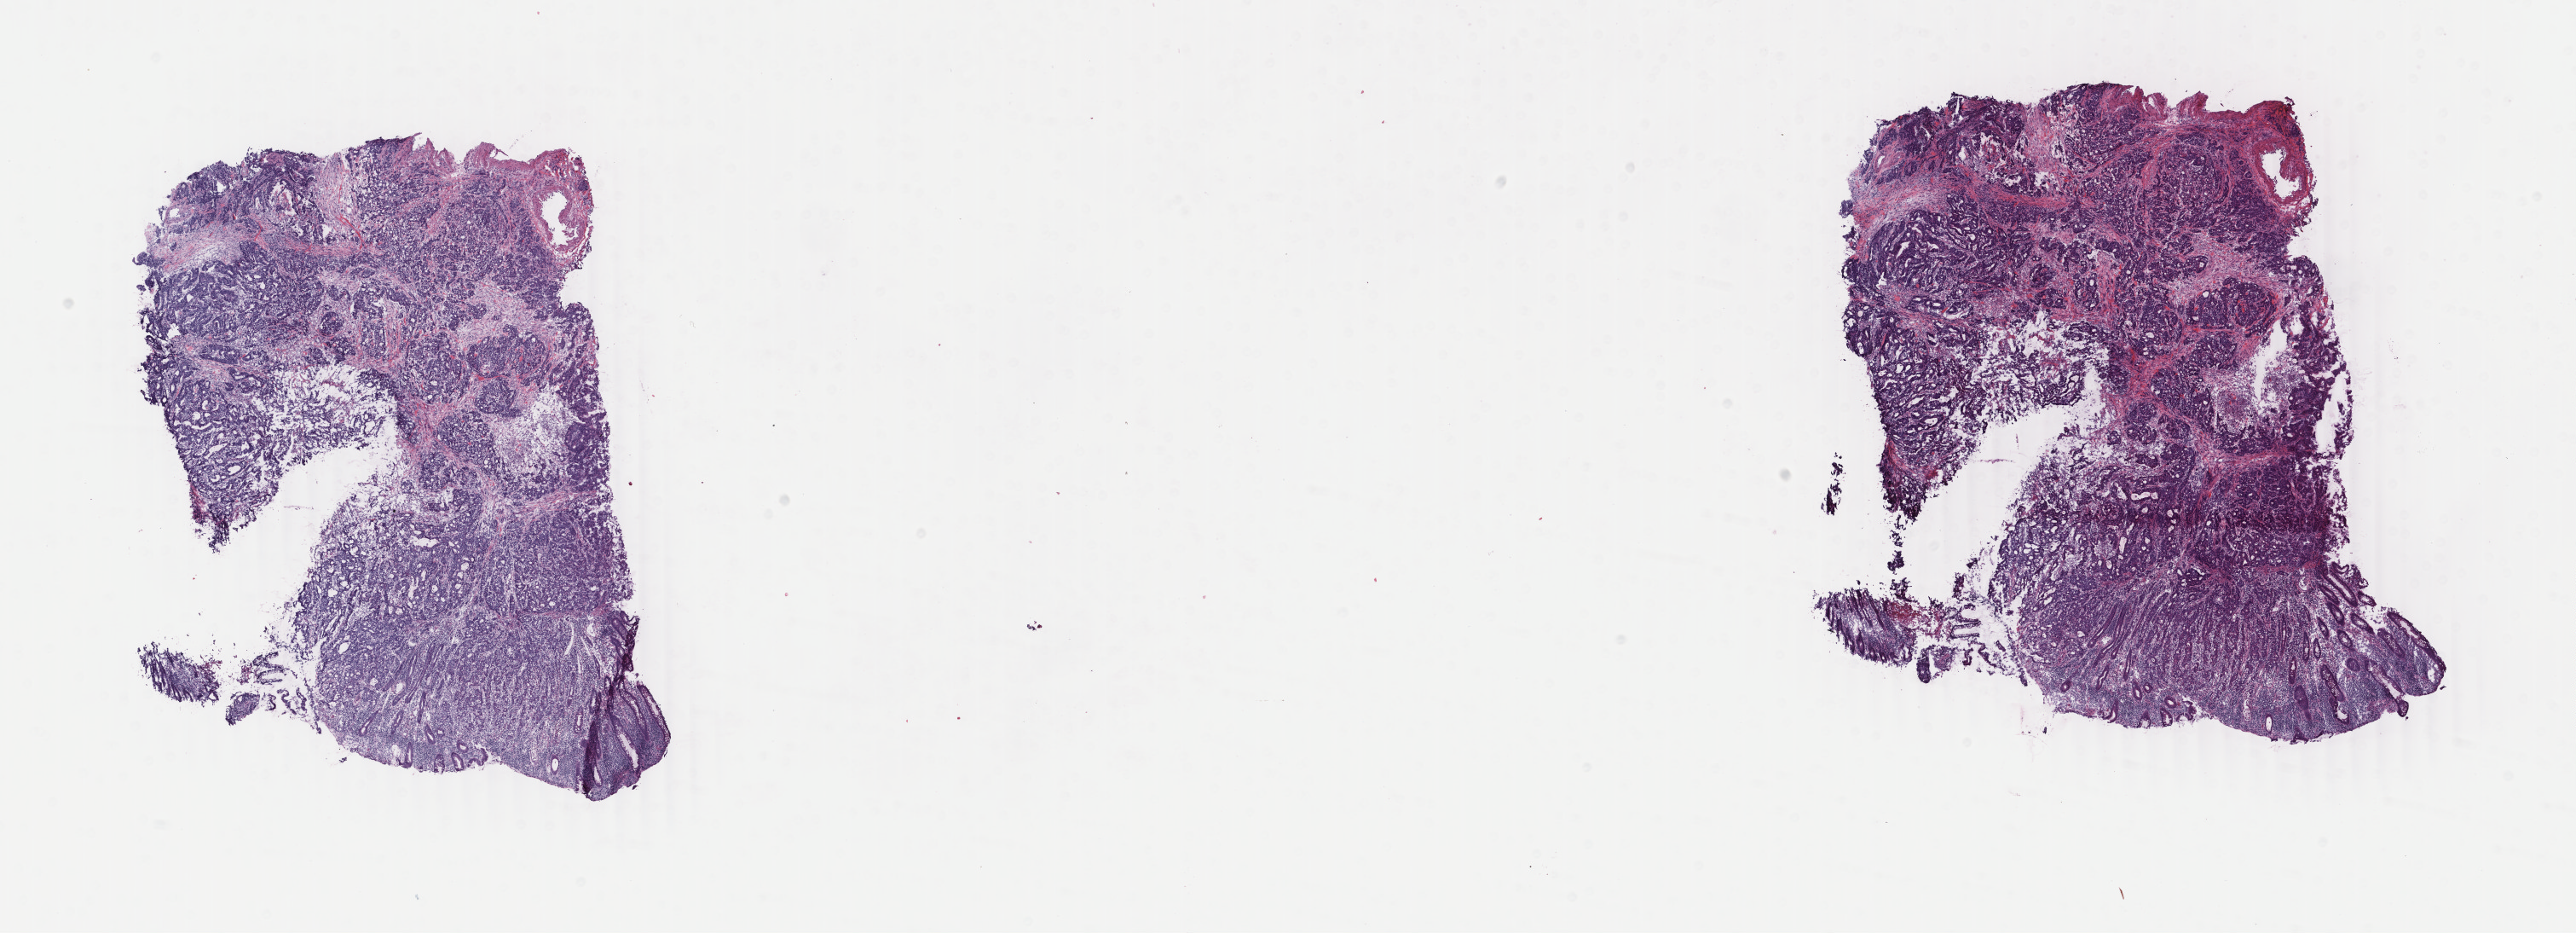
H&E-stained whole-slide image, shown as a low-resolution overview of the whole scanned area (about 24.0 x 8.7 mm, slide scanned at 40x). Frozen section. Colon, primary tumour sample. Patient: female, age at initial diagnosis 88 years. Slide review estimates, as recorded: tumour cells 75%, tumour nuclei 80%, normal cells 6%, stromal cells 15%, necrosis 4%. Infiltration values recorded for this section: lymphocyte infiltration 3%, monocyte infiltration 1%, neutrophil infiltration 3%.
• AJCC pathologic stage: II (5th edition)
• lymph nodes positive (case pathology): 0 of 18 examined
• diagnosis: Adenocarcinoma, NOS (cecum)